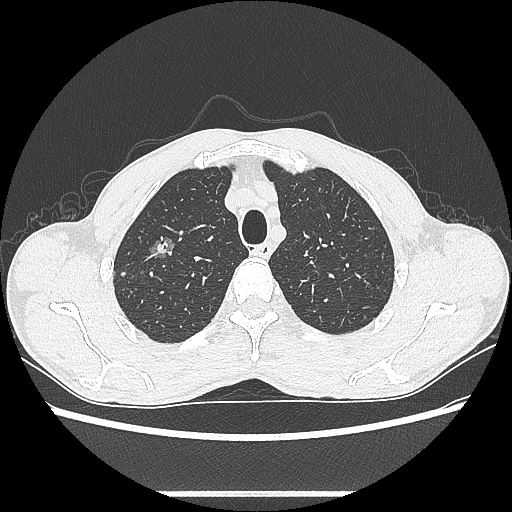
Chest CT, one axial slice. Position 487 of 601 along the scan axis. Lung window (W 1500 / L -600 HU). 512 × 512 image matrix, field of view 357 × 357 mm. Male patient, age 54 years. Case-level facts recorded for this patient, not image findings: clinical TNM (as recorded): T1a N0 M0.
Annotated regions visible in this slice (bounding box drawn by a radiologist):
- lung tumour (recorded histology: adenocarcinoma): bounding box [x1, y1, x2, y2] px = [147, 231, 178, 265]